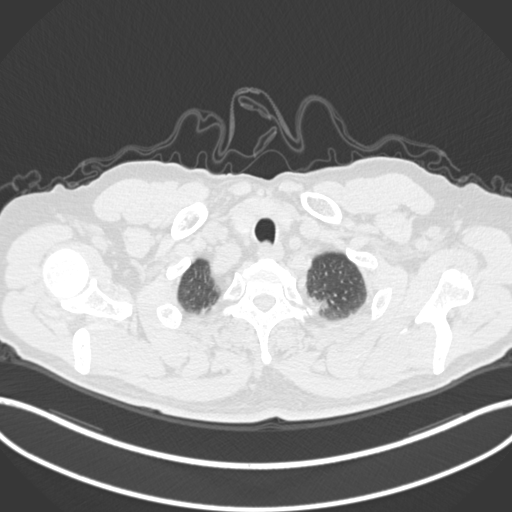
Chest CT, one axial slice. Slice 296 of 306 in the series (ordered by position). Reconstruction kernel B30f. Lung window (W 1500 / L -600 HU). 512 × 512 image matrix, field of view 400 × 400 mm. Male patient, age 64 years. Case-level facts recorded for this patient, not image findings: clinical TNM (as recorded): T1c N0 M0.
Structures marked on this image (rectangle marked by the reading radiologist):
- lung tumour (recorded histology: adenocarcinoma): bounding box [x1, y1, x2, y2] px = [310, 290, 335, 318]